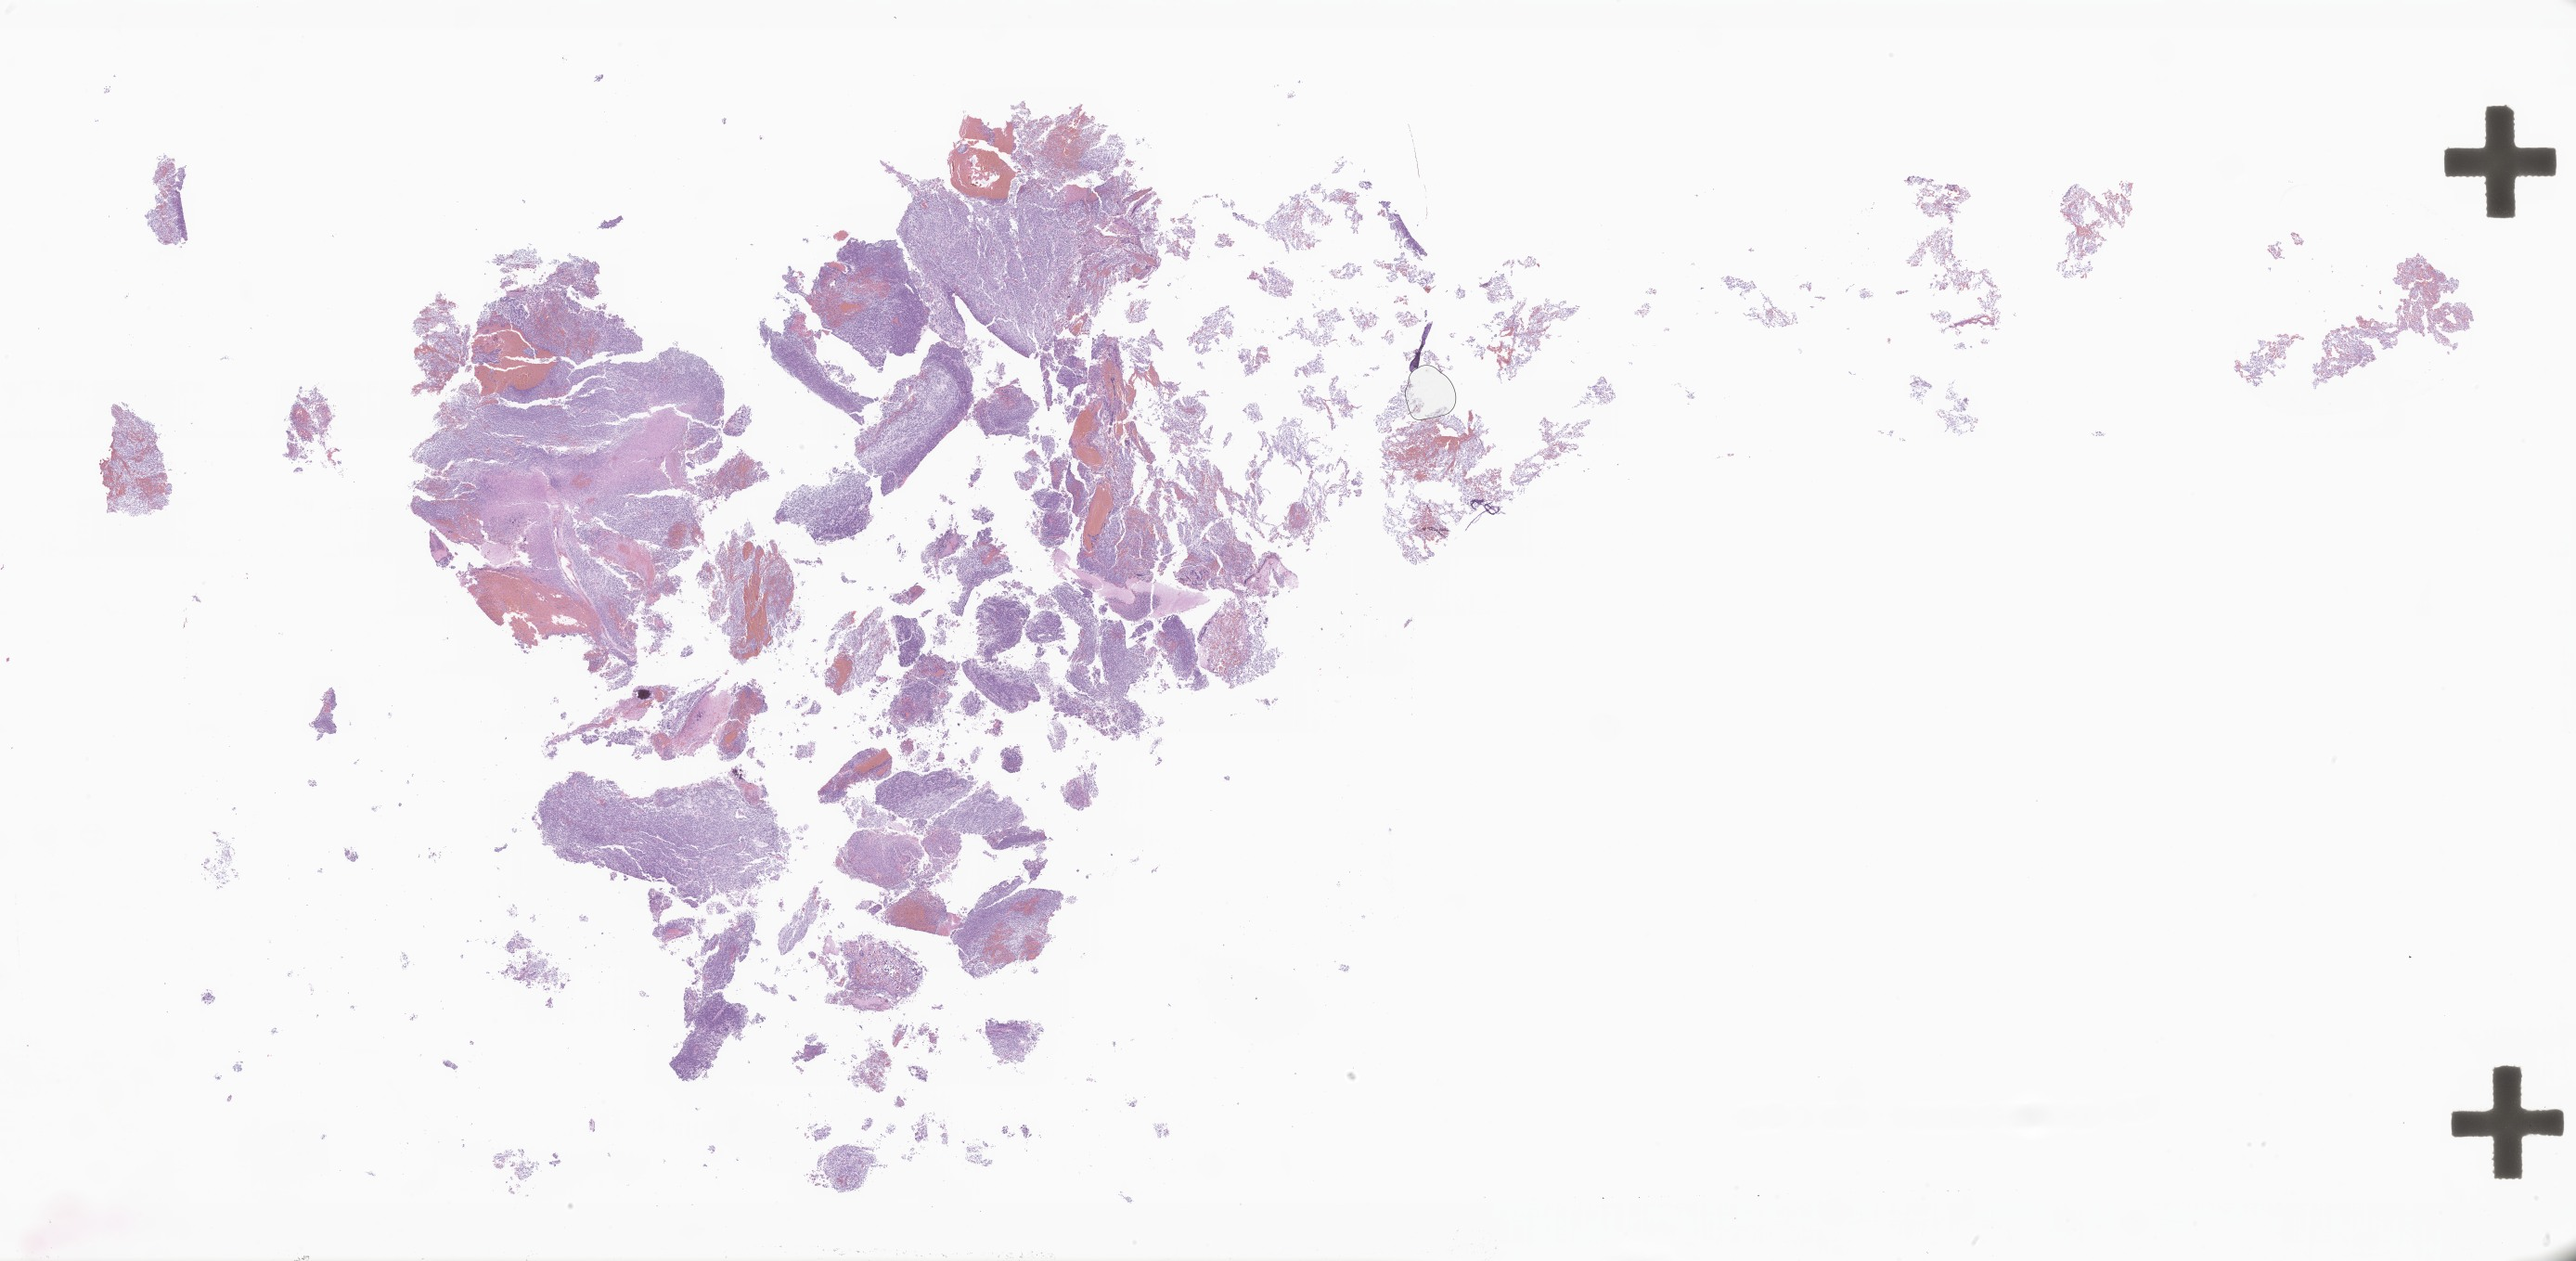
Whole-slide image, hematoxylin and eosin (H&E) stain of tumor tissue from the brain — shown as a low-resolution overview of the whole scanned area (about 46.8 x 22.9 mm). Formalin-fixed, paraffin-embedded (FFPE) tissue. Patient: female, age 116 months (9 years 8 months).
* recorded diagnosis: Neoplasm, malignant